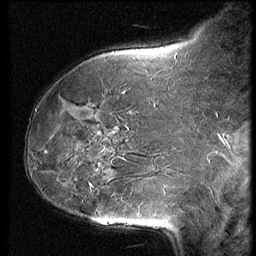
Breast MRI (dynamic contrast-enhanced), one sagittal slice. Slice 22 of 62 in the series (ordered by position). 3 images stored at this slice position (order not interpretable as contrast timing). 1.5 T. TE 4.2 ms, TR 9 ms. 2.5 mm slice thickness. 256 × 256 image matrix, field of view 180 × 180 mm. Patient: female, 50 years. From the clinical record (not read from this slice): setting: breast cancer imaged before/during neoadjuvant chemotherapy; receptor status: HR-positive, HER2-negative.
Annotated regions visible in this slice (semi-automatic segmentation, software-assisted and operator-edited):
- analysis volume of interest (the breast-tissue region the enhancement analysis was run in; not a lesion): bounding box [x1, y1, x2, y2] px = [59, 125, 139, 232]
- tumour enhancement mask (voxels above the 140 % enhancement threshold inside the analysis volume of interest): [105, 220, 108, 222]